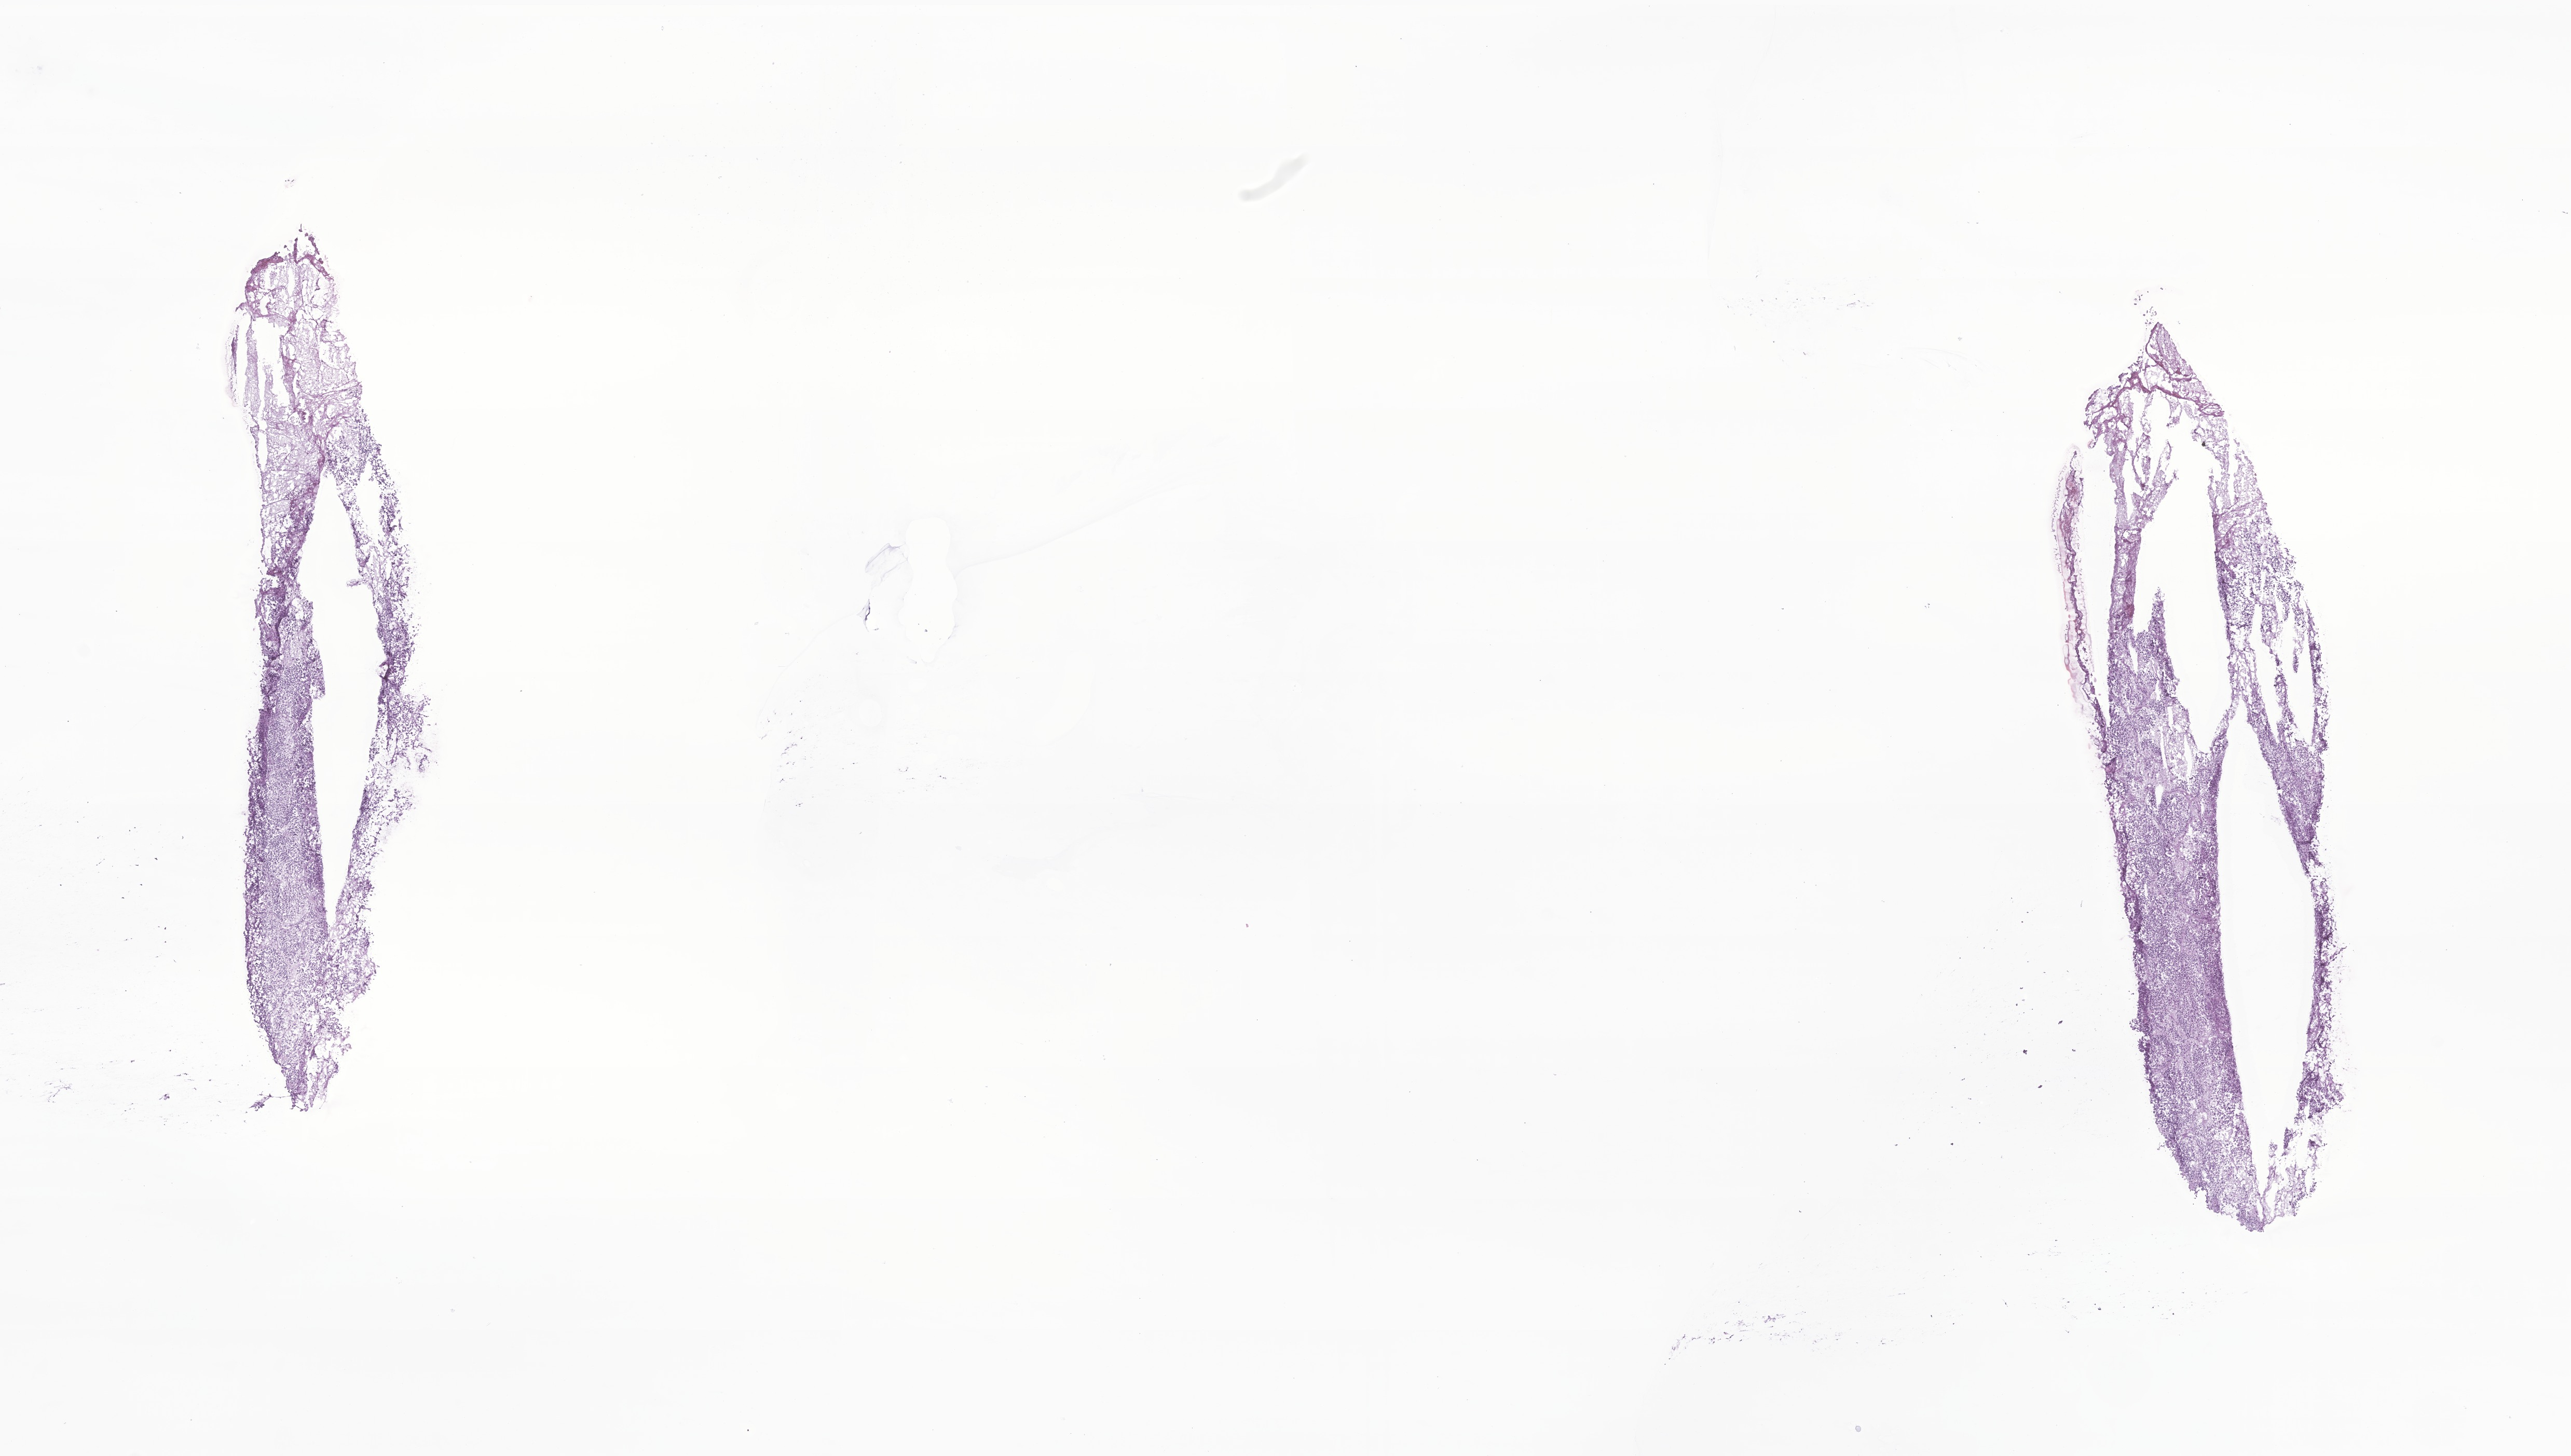
Hematoxylin and eosin (H&E) whole-slide image of tumor tissue from the brain, shown as a low-resolution overview of the whole scanned area (about 20.9 x 11.8 mm), frozen section. Patient male; age 240 months (20 years).
Diagnosis: Neuroblastoma, NOS.